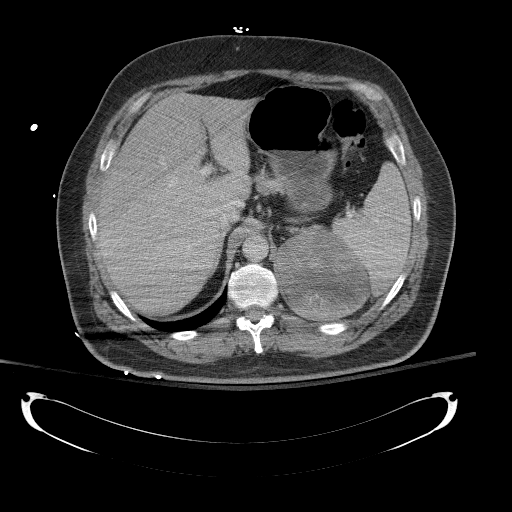
Contrast-enhanced abdominal CT, one axial slice. Slice 92 of 154 in the series (ordered by position). 120 kVp. Intravenous contrast given. Soft-tissue window (W 400 / L 40 HU). 512 × 512 image matrix, field of view 467 × 467 mm. Male patient, age 43 years. Case-level facts recorded for this patient, not image findings: diagnosis: adrenocortical carcinoma; tumour side: left adrenal; tumour size at pathology: 9.8 cm; Ki-67 index: 30 %; stage (as recorded): 2.
Outlined on this slice (semi-automatically segmented with operator editing):
- mass: bounding box (x1, y1, x2, y2) in pixels: (278, 225, 368, 319)